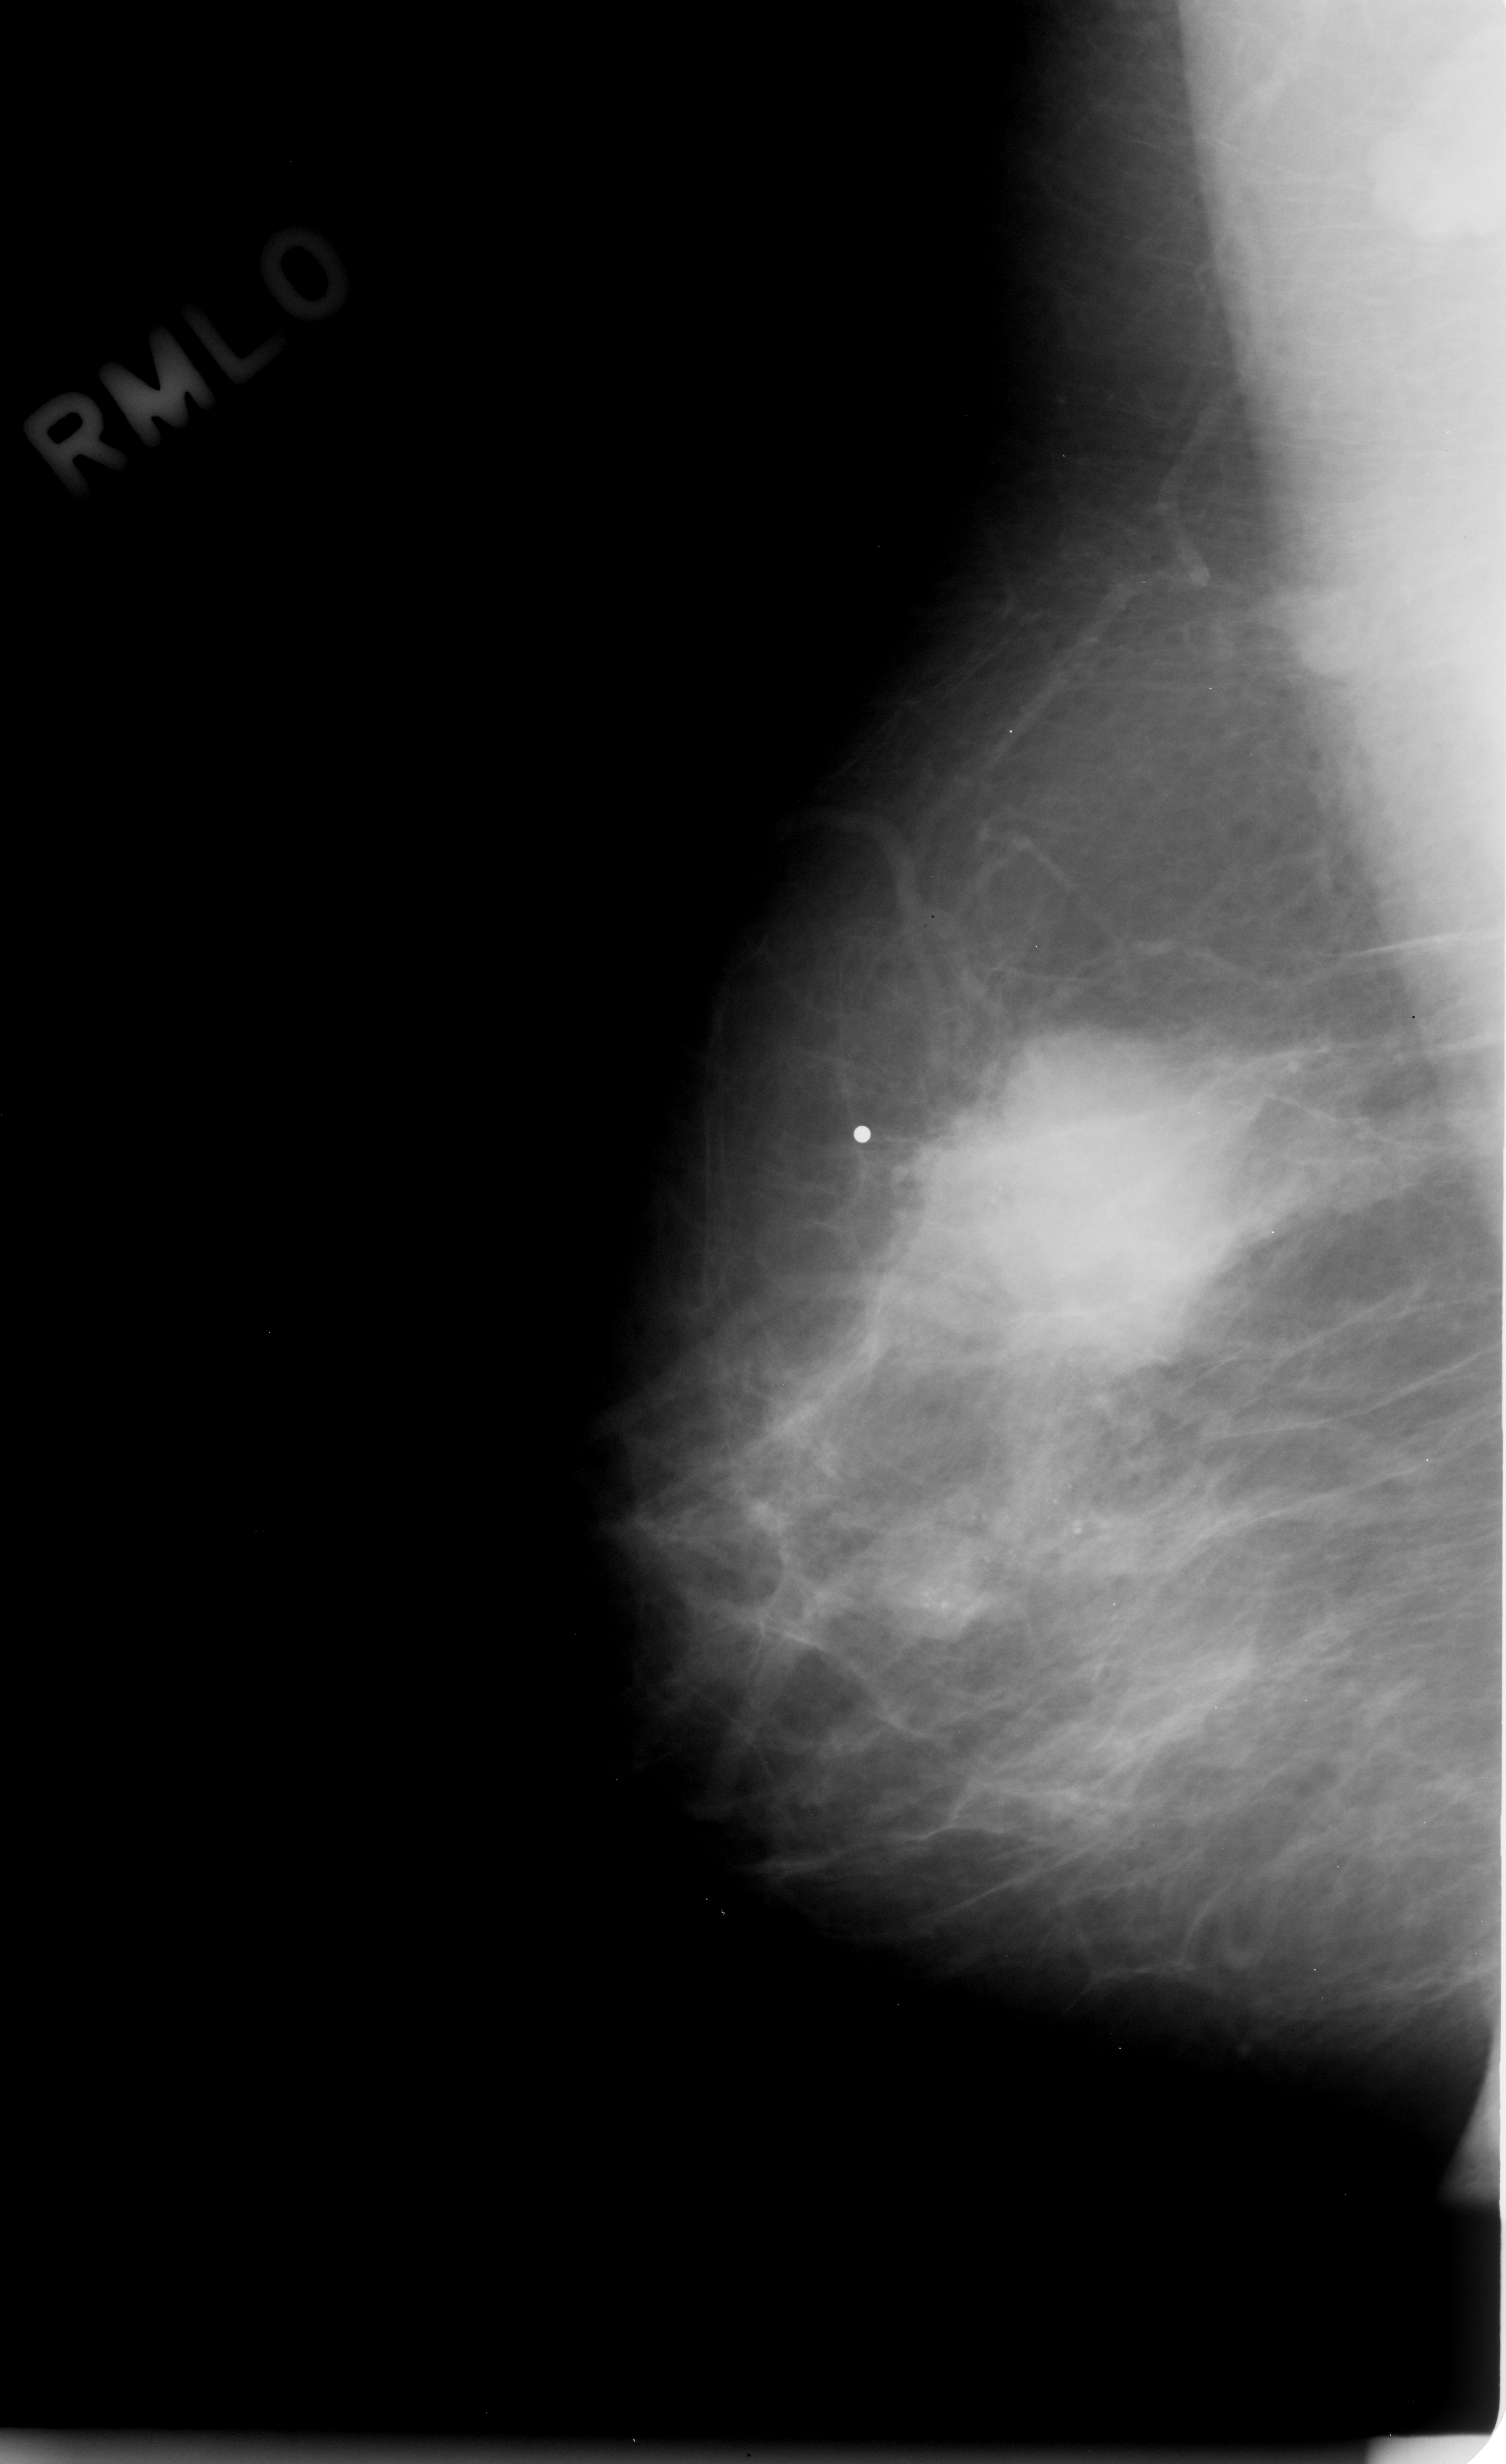
Digitized screen-film mammogram; right breast; MLO view; 1506 × 2464 image matrix.
Expert-marked regions of interest on this film, with their recorded descriptors:
- Finding 1 of 2: mass, shape irregular, margins microlobulated; BI-RADS assessment category 5; pathology result (as recorded, not read from the image): malignant: bounding box <1240,575,1358,686> (left, top, right, bottom; pixels)
- Finding 2 of 2: mass, shape irregular, margins microlobulated; BI-RADS assessment category 5; subtlety rating 5 on a 1 (subtle) to 5 (obvious) scale; pathology result (as recorded, not read from the image): malignant: <1350,82,1506,275>